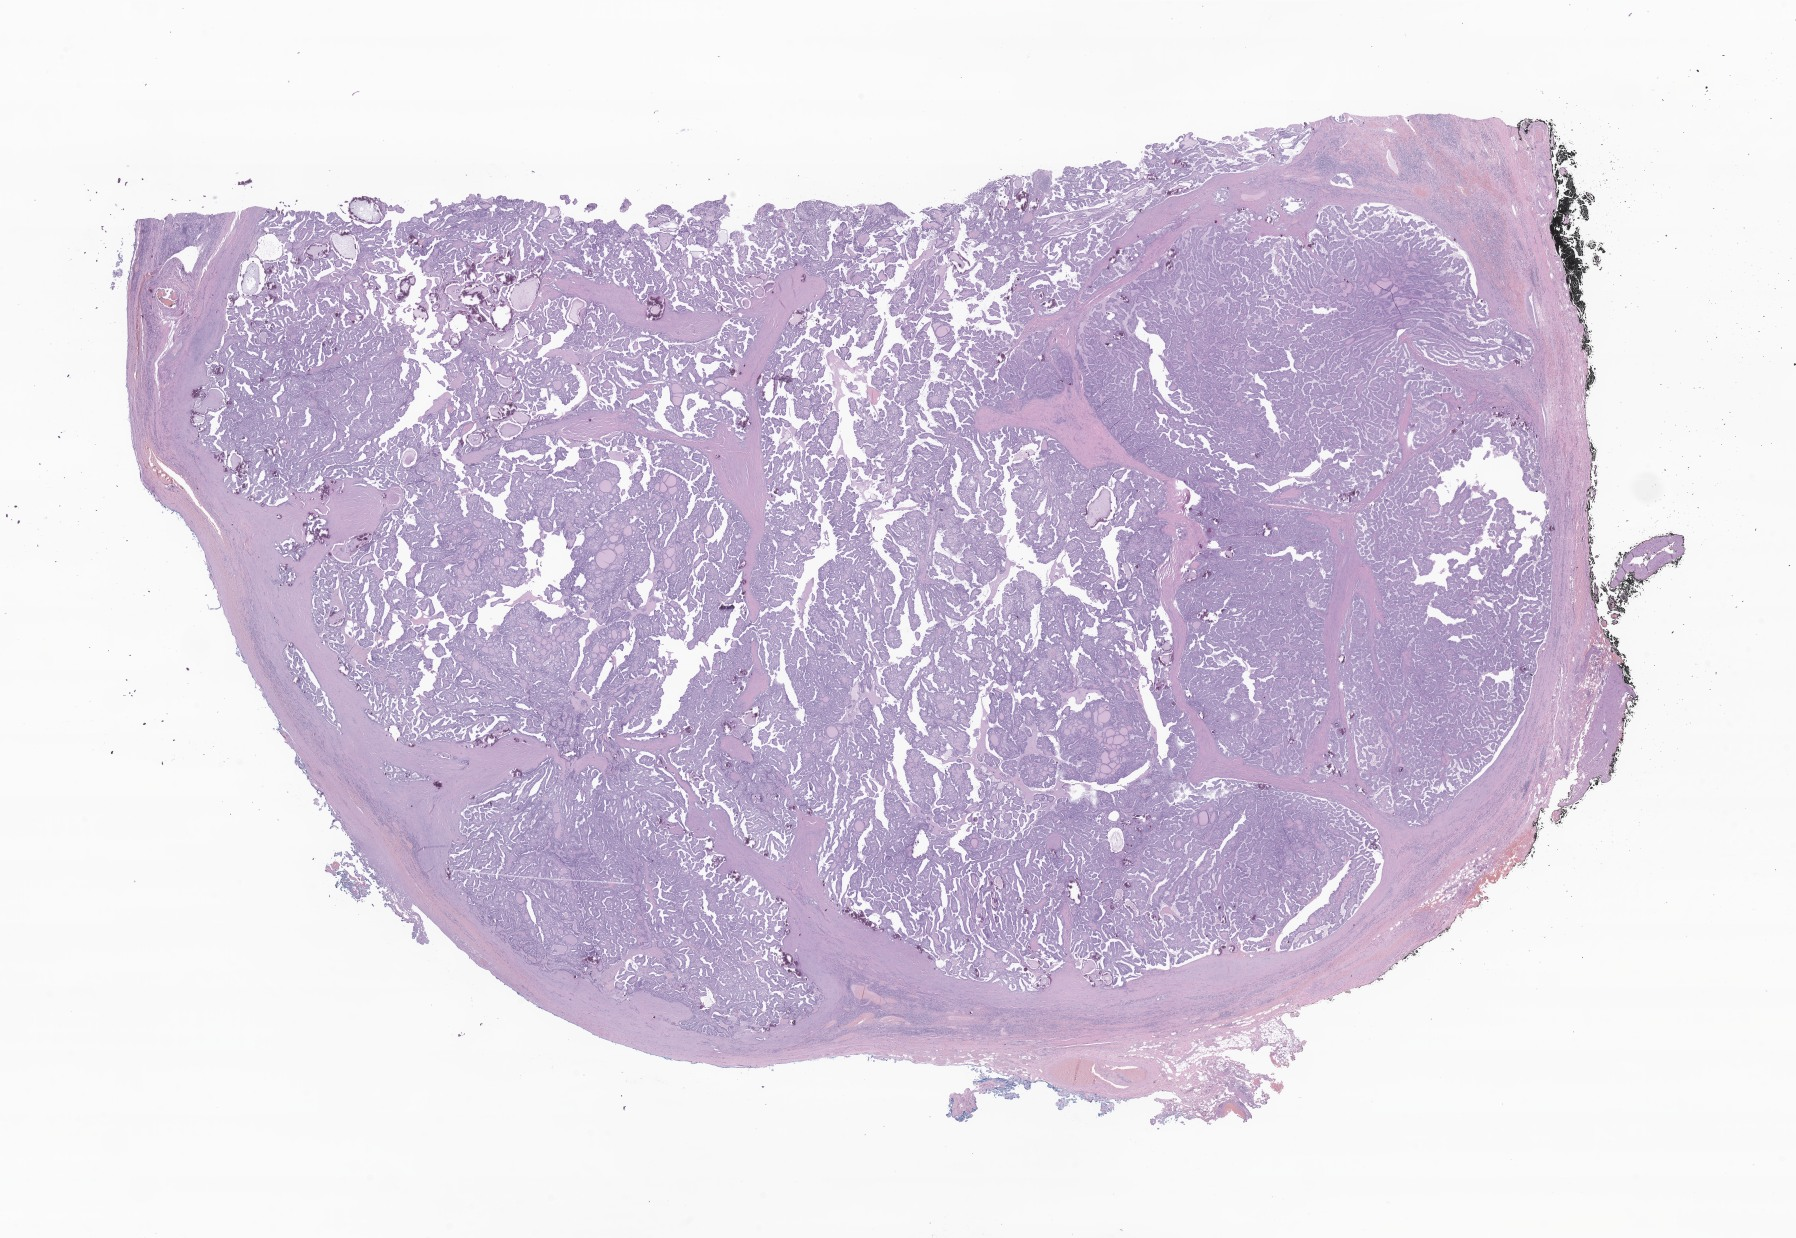
Whole-slide image, hematoxylin and eosin (H&E) stain of tumor tissue from the thyroid — a low-resolution overview of the entire scanned area, about 30.3 x 20.9 mm. Formalin-fixed paraffin-embedded section. Female patient, age 185 months (15 years 5 months).
Diagnosis (ICD-O-3 morphology term): Papillary carcinoma, NOS.